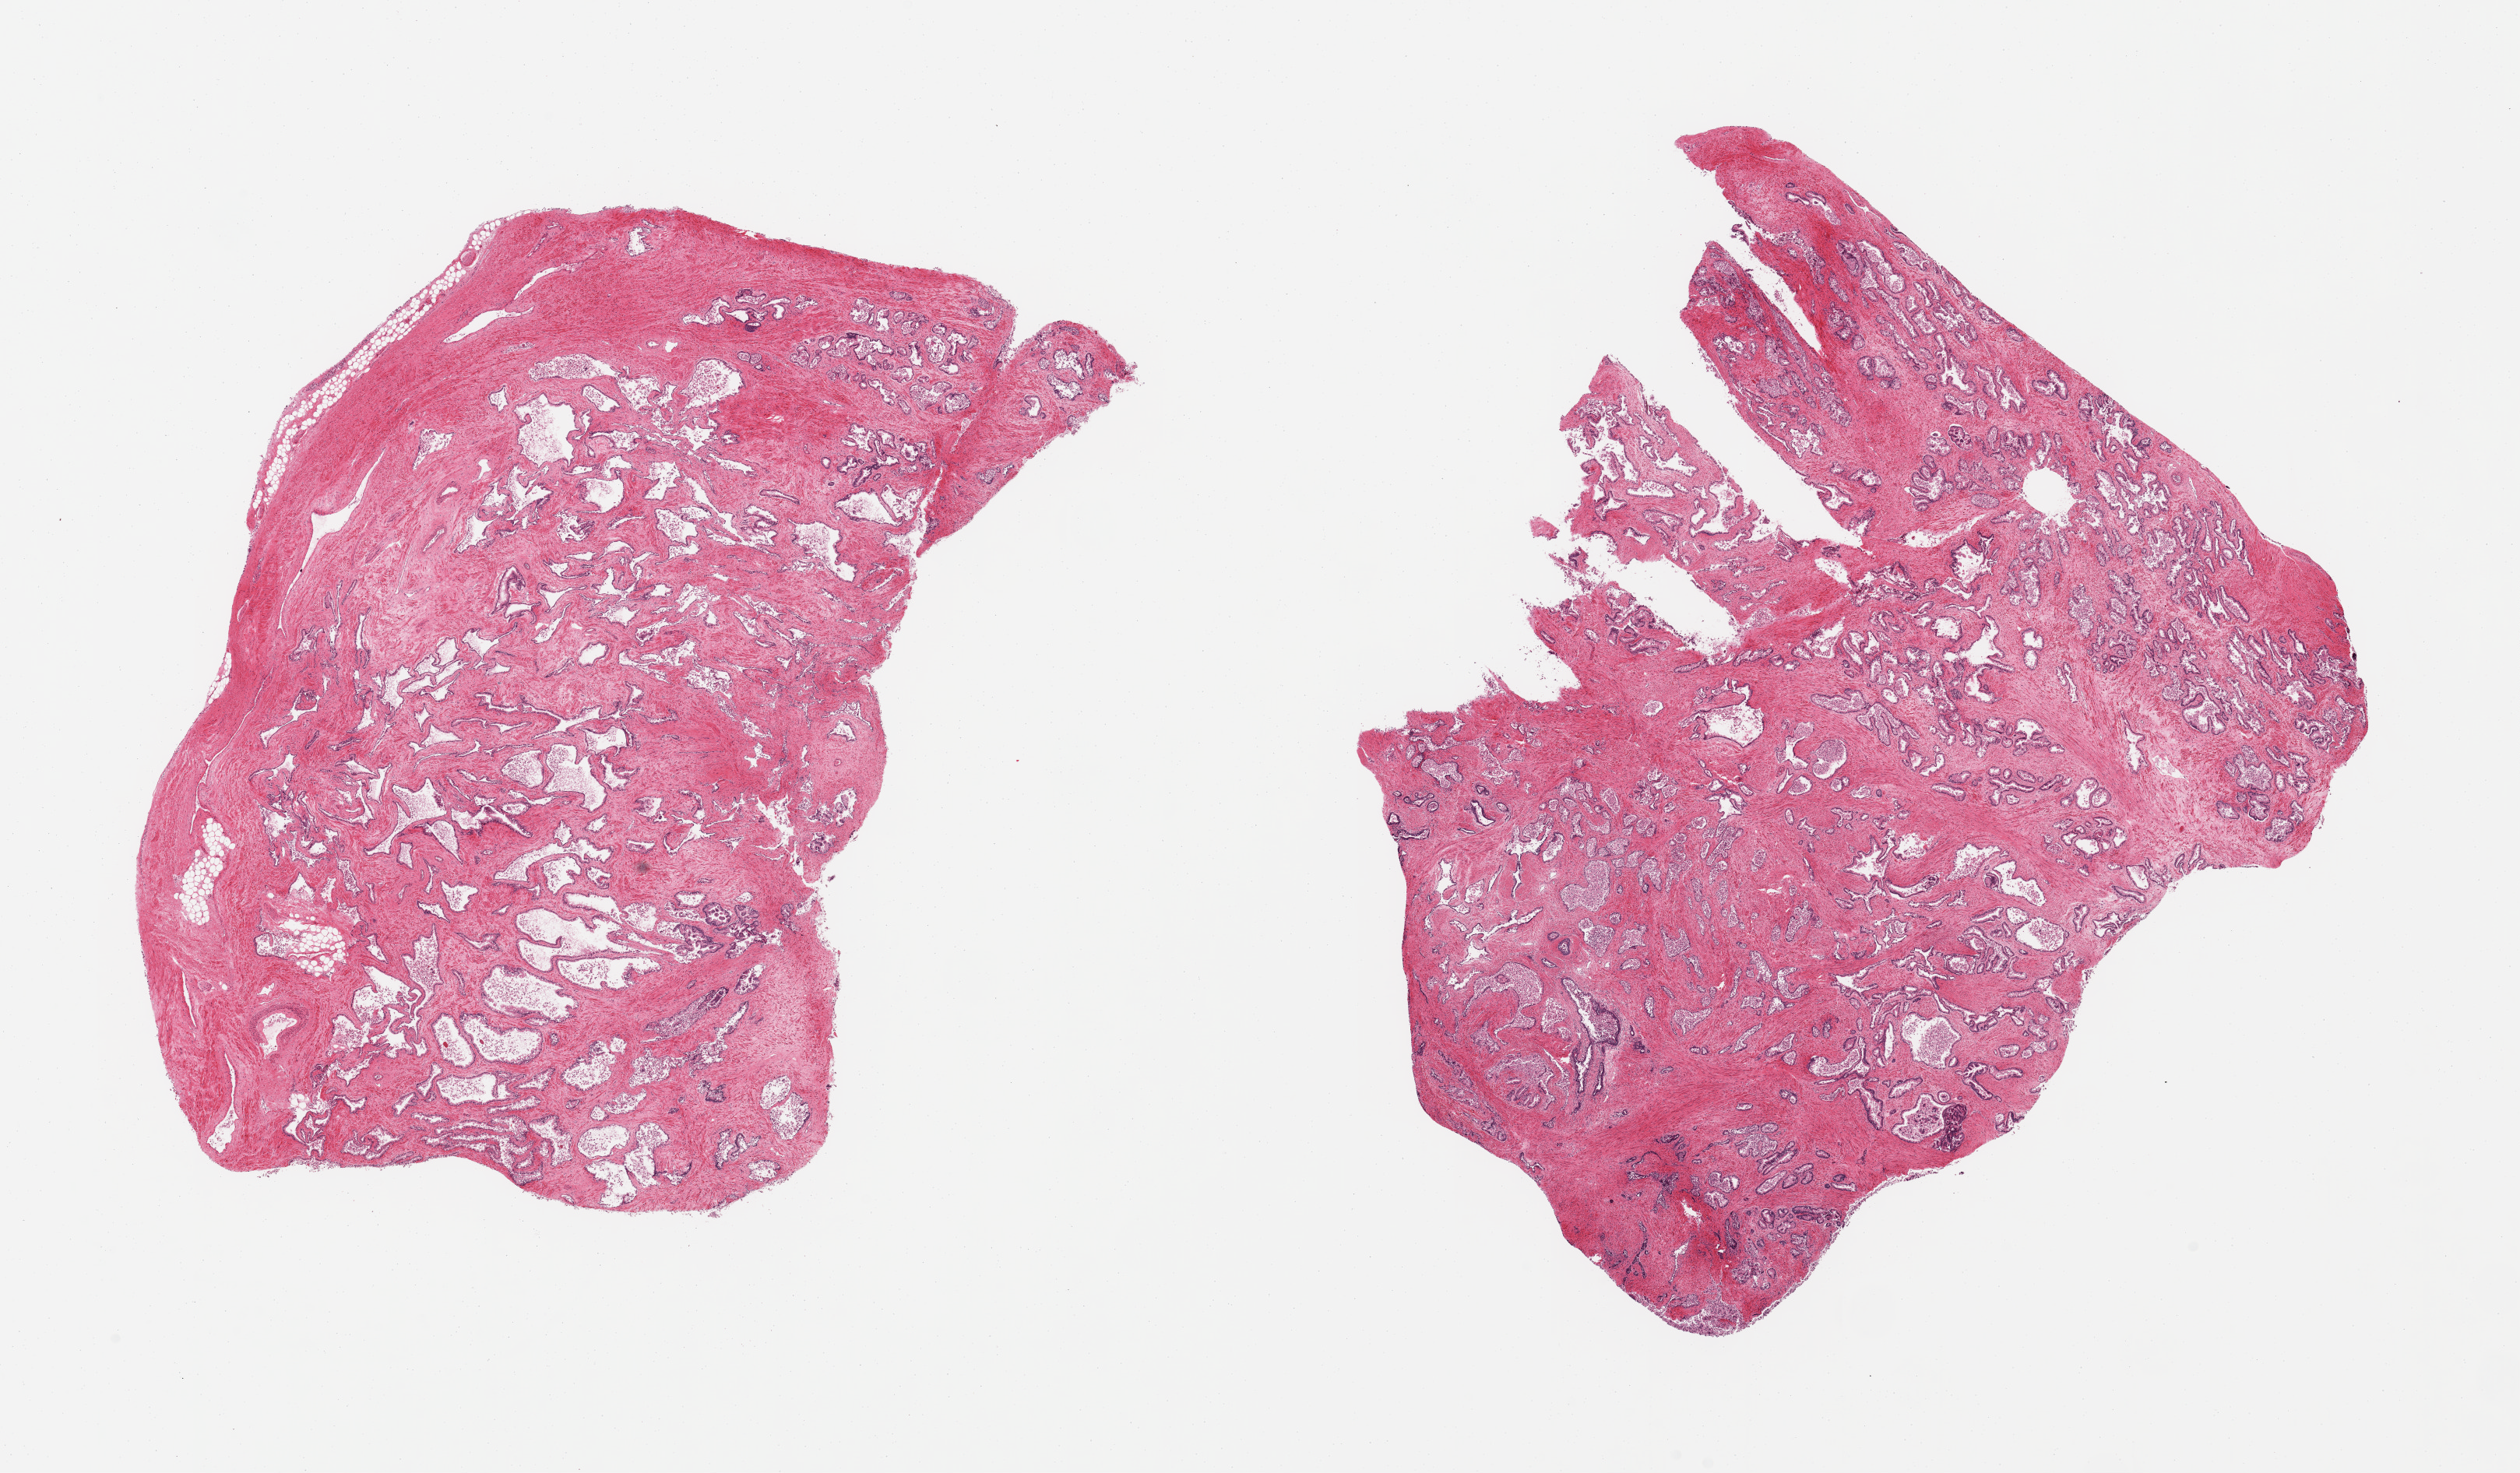
Digitized hematoxylin and eosin (H&E)-stained section, brightfield — shown as a low-resolution overview of the whole scanned area (about 25.6 x 15.0 mm). PAXgene-fixed paraffin-embedded (PFPE) section. Target tissue: prostate. Tissue donor sample. Donor sex: male.
Reviewer comment on this tissue sample: 2 pieces; glands with sloughed epithelium and stroma.